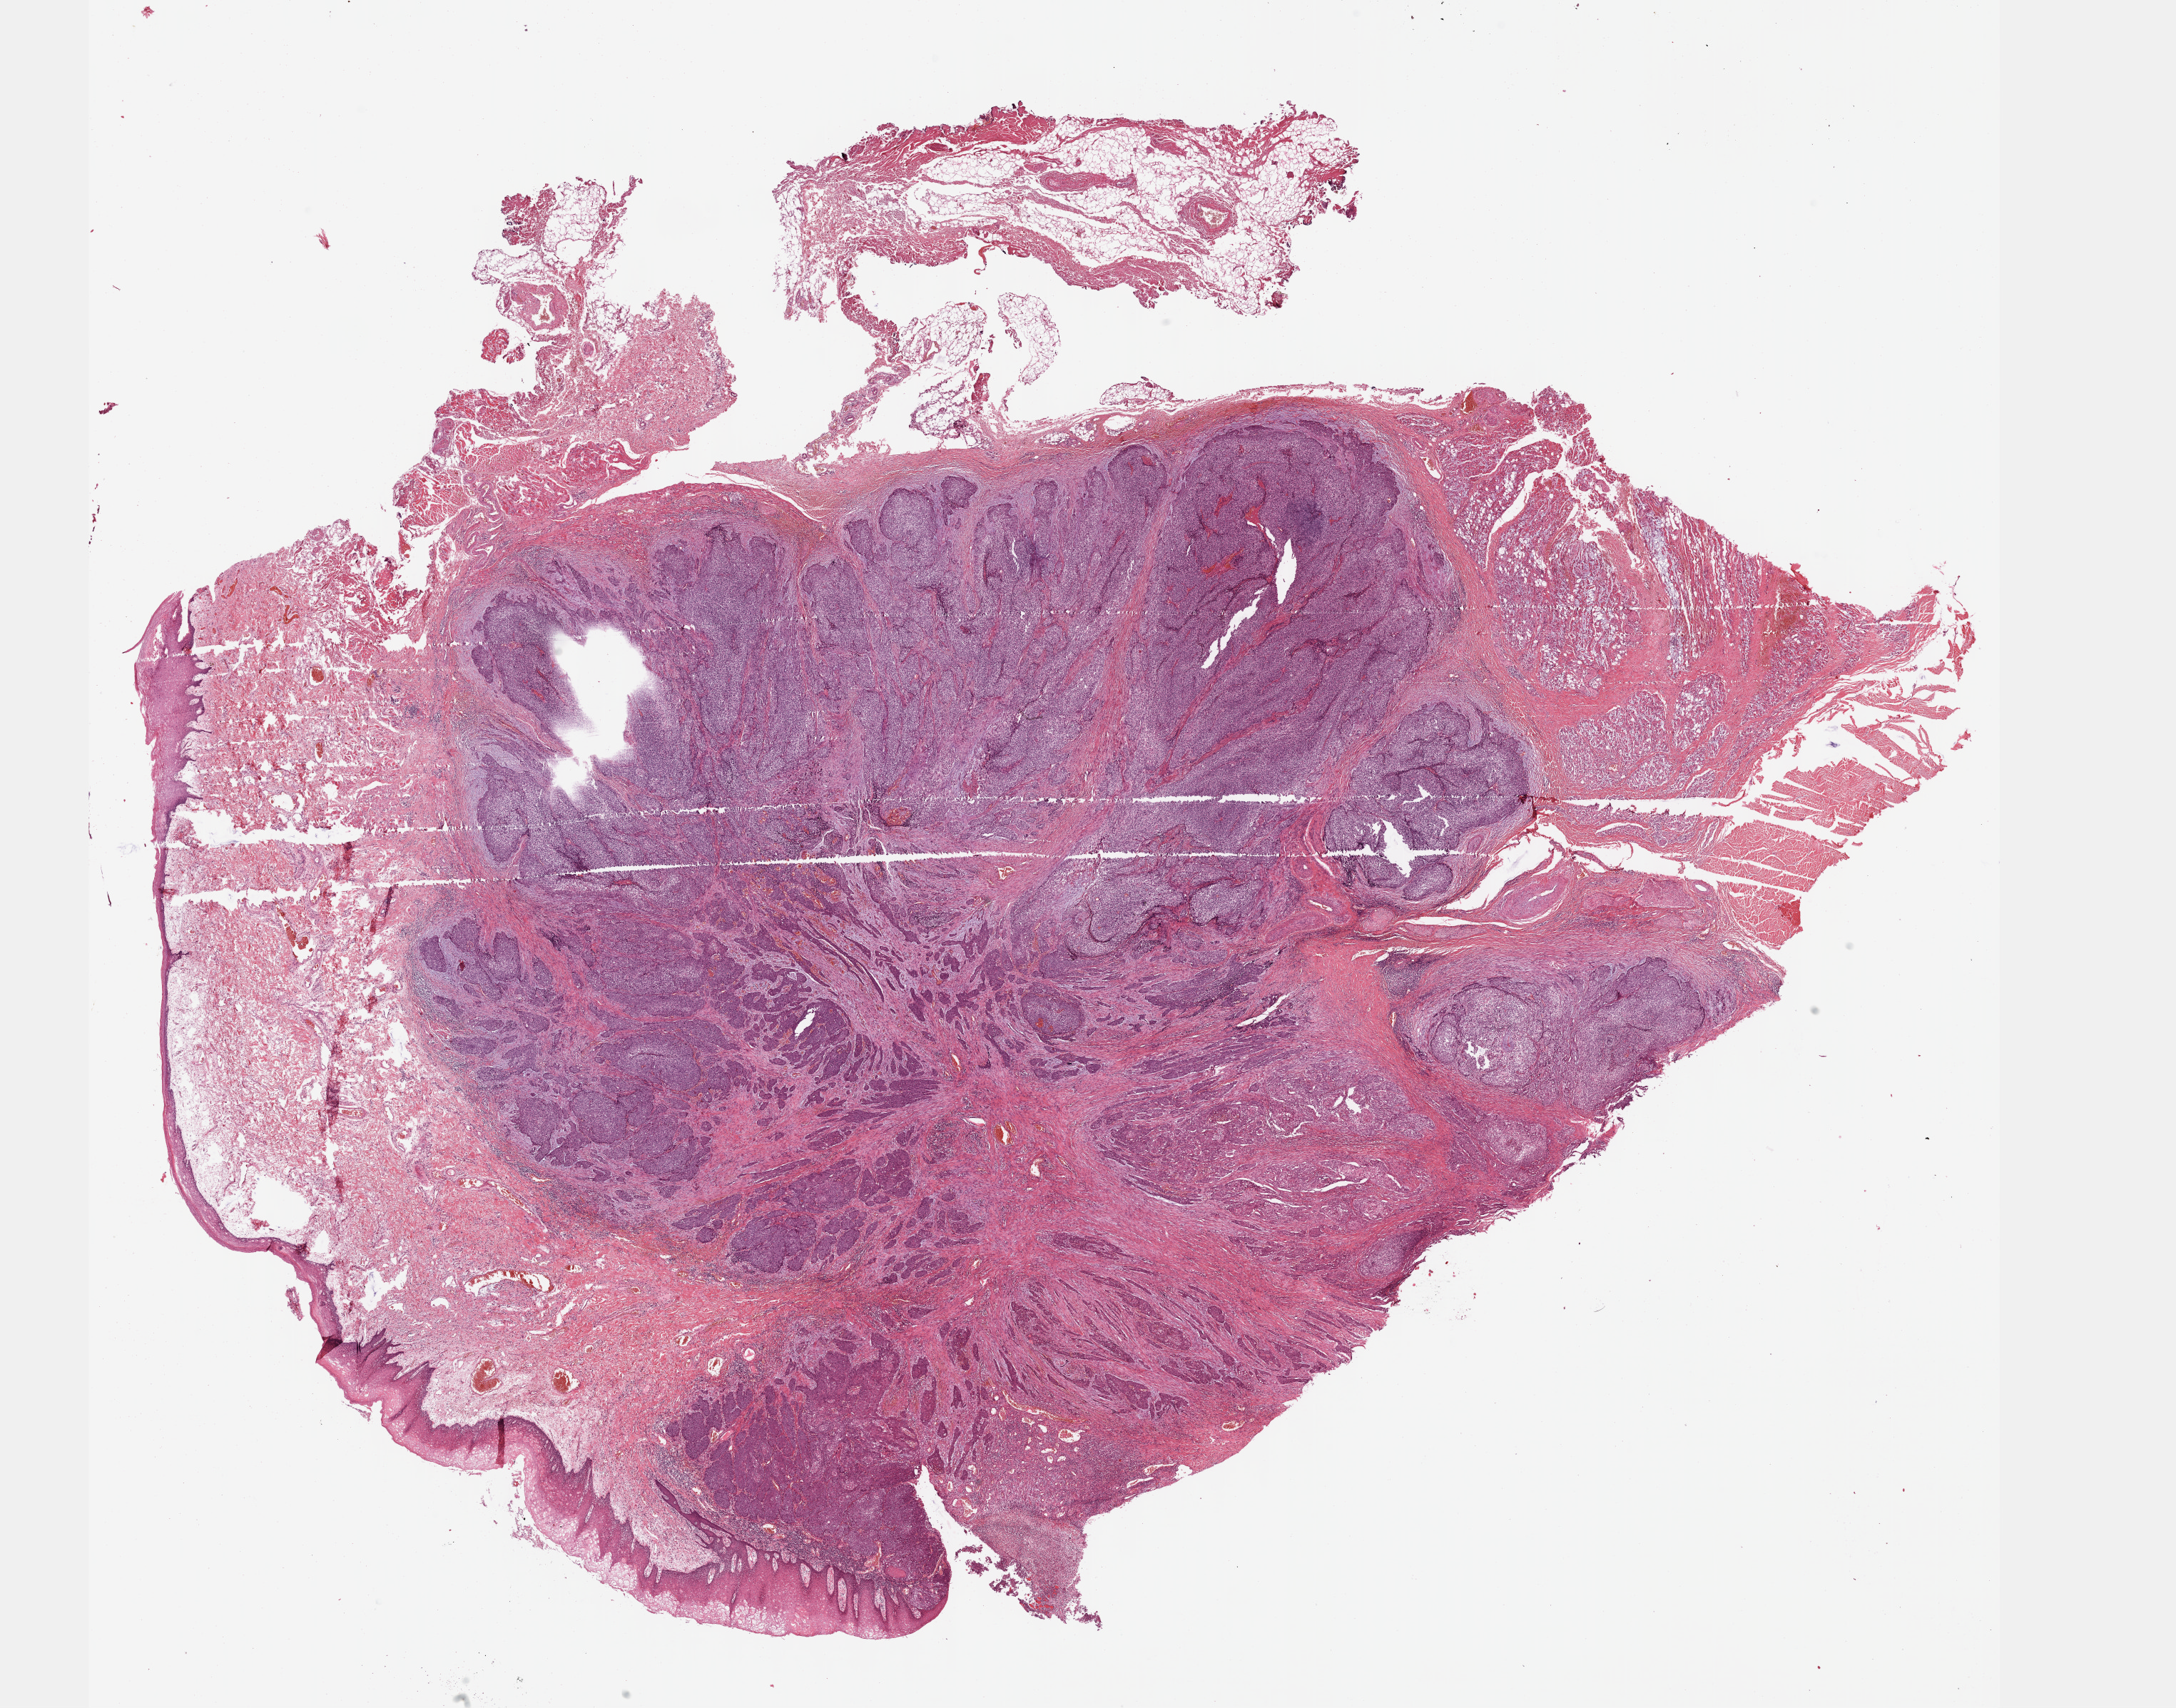
Digitized H&E tissue section (whole slide), a low-resolution overview of the entire scanned area, about 24.6 x 19.3 mm (slide scanned at 40x); formalin-fixed paraffin-embedded (FFPE) diagnostic section; primary tumour sample from the head and neck. Female, age 66 years at initial diagnosis. Histologic grade: G2 (moderately differentiated).
Pathologic diagnosis: Squamous cell carcinoma, NOS (cheek mucosa). AJCC pathologic stage: IVA (7th edition).